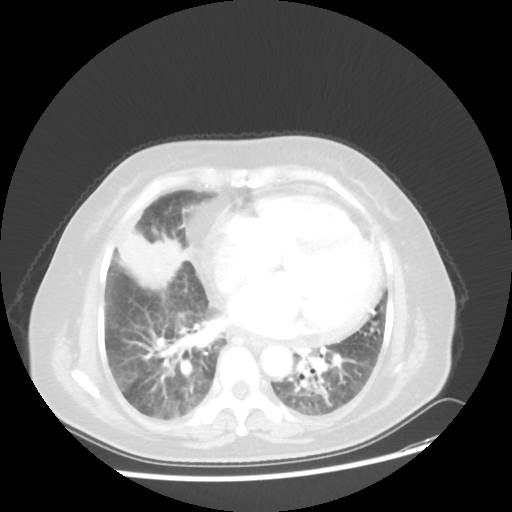
Chest CT, one axial slice; slice 18 of 45 in the series (ordered by position); reconstruction kernel STANDARD; lung window (W 1500 / L -600 HU); 5 mm slice thickness; 512 × 512 image matrix, field of view 359 × 359 mm. Patient: female, 67 years. From the clinical record (not read from this slice): clinical TNM (as recorded): T2a N3 M1a.
Outlined on this slice (rectangle marked by the reading radiologist):
- lung tumour (recorded histology: adenocarcinoma): bounding box <119,231,186,294> (left, top, right, bottom; pixels)